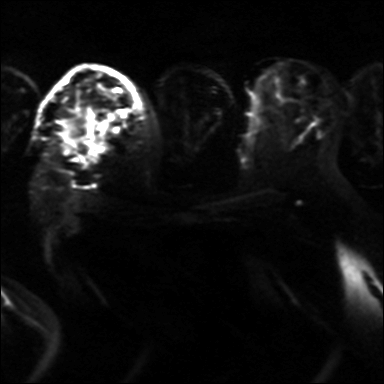
Breast MRI, one axial slice. Position 23 of 36 along the scan axis. Diffusion-weighted series; image 2 of 4 stored at this slice position (different b-values; order by instance number). 3 T. 4 mm slice thickness. 384 × 384 image matrix. Female patient.
Annotated regions visible in this slice (outlined manually by an expert reader):
- tumour on diffusion-weighted imaging: bounding box (x1, y1, x2, y2) in pixels: (64, 113, 113, 147)